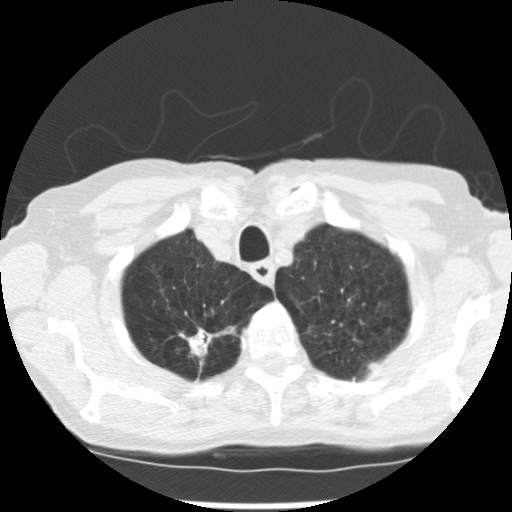
Chest CT (low-dose screening protocol), one axial image. Baseline annual screen. Lung window (W 1500 / L -600 HU). 2.5 mm slice thickness. Slice 30 of 265 in the series. Female participant, aged 72 years at enrolment. Current smoker at enrolment.
Expert reader's lesion annotation, bounding box (x1, y1, x2, y2) in pixels: (175, 314, 231, 357). The screening reader recorded 3 non-calcified nodules or masses ≥4 mm on this exam; which of them this box marks is not recorded. Later outcome: lung cancer diagnosed 50 days after this screen — adenocarcinoma, NOS, right upper lobe, moderately differentiated (G2), stage IB (AJCC 6th edition), 22 mm at pathology.